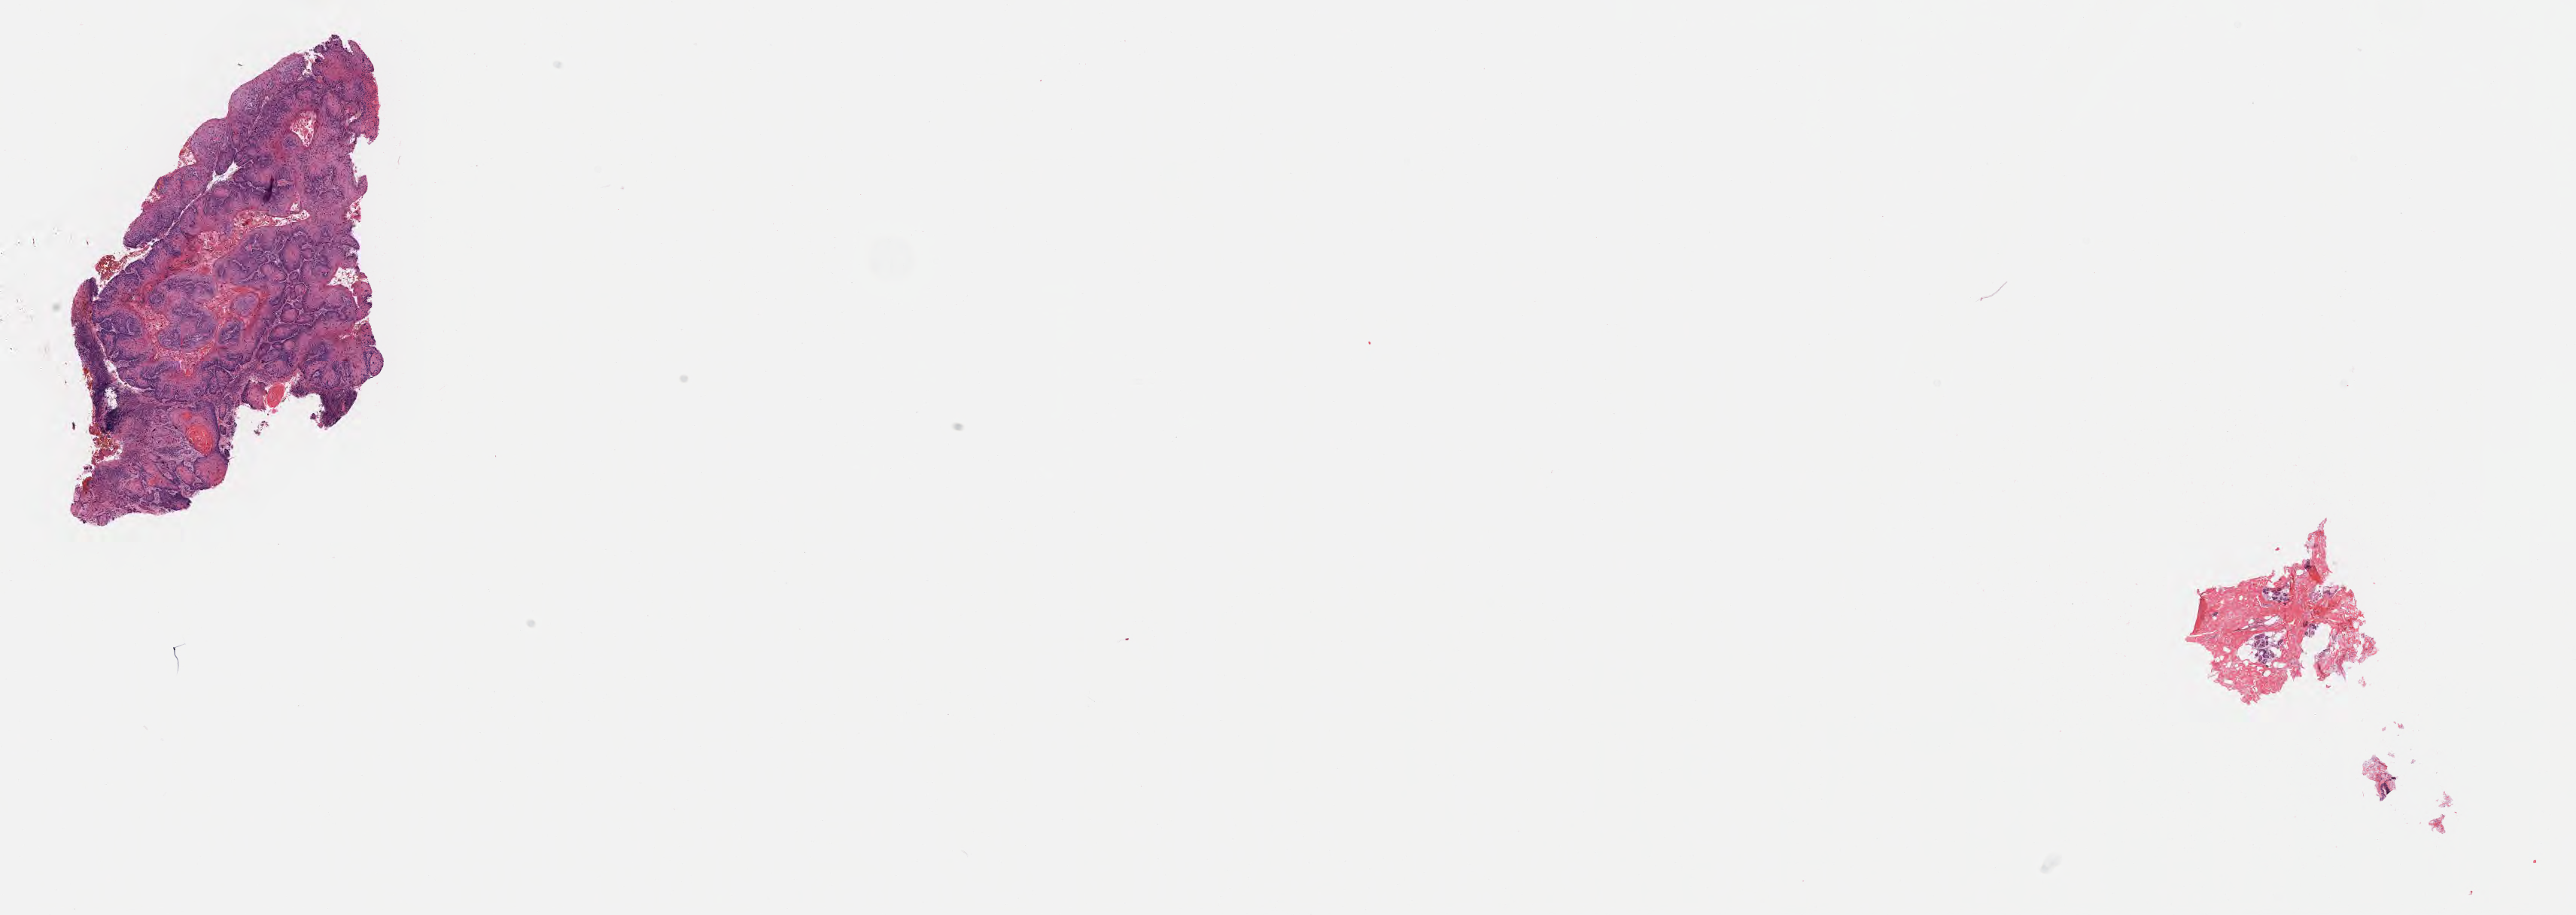
Whole-slide image, H&E stain — whole scanned area (about 27.7 x 9.8 mm) shown as a low-resolution overview. Specimen: tumor tissue. Site: cervix. Patient female; aged 65.
• histologic diagnosis: Squamous cell carcinoma, keratinizing, NOS